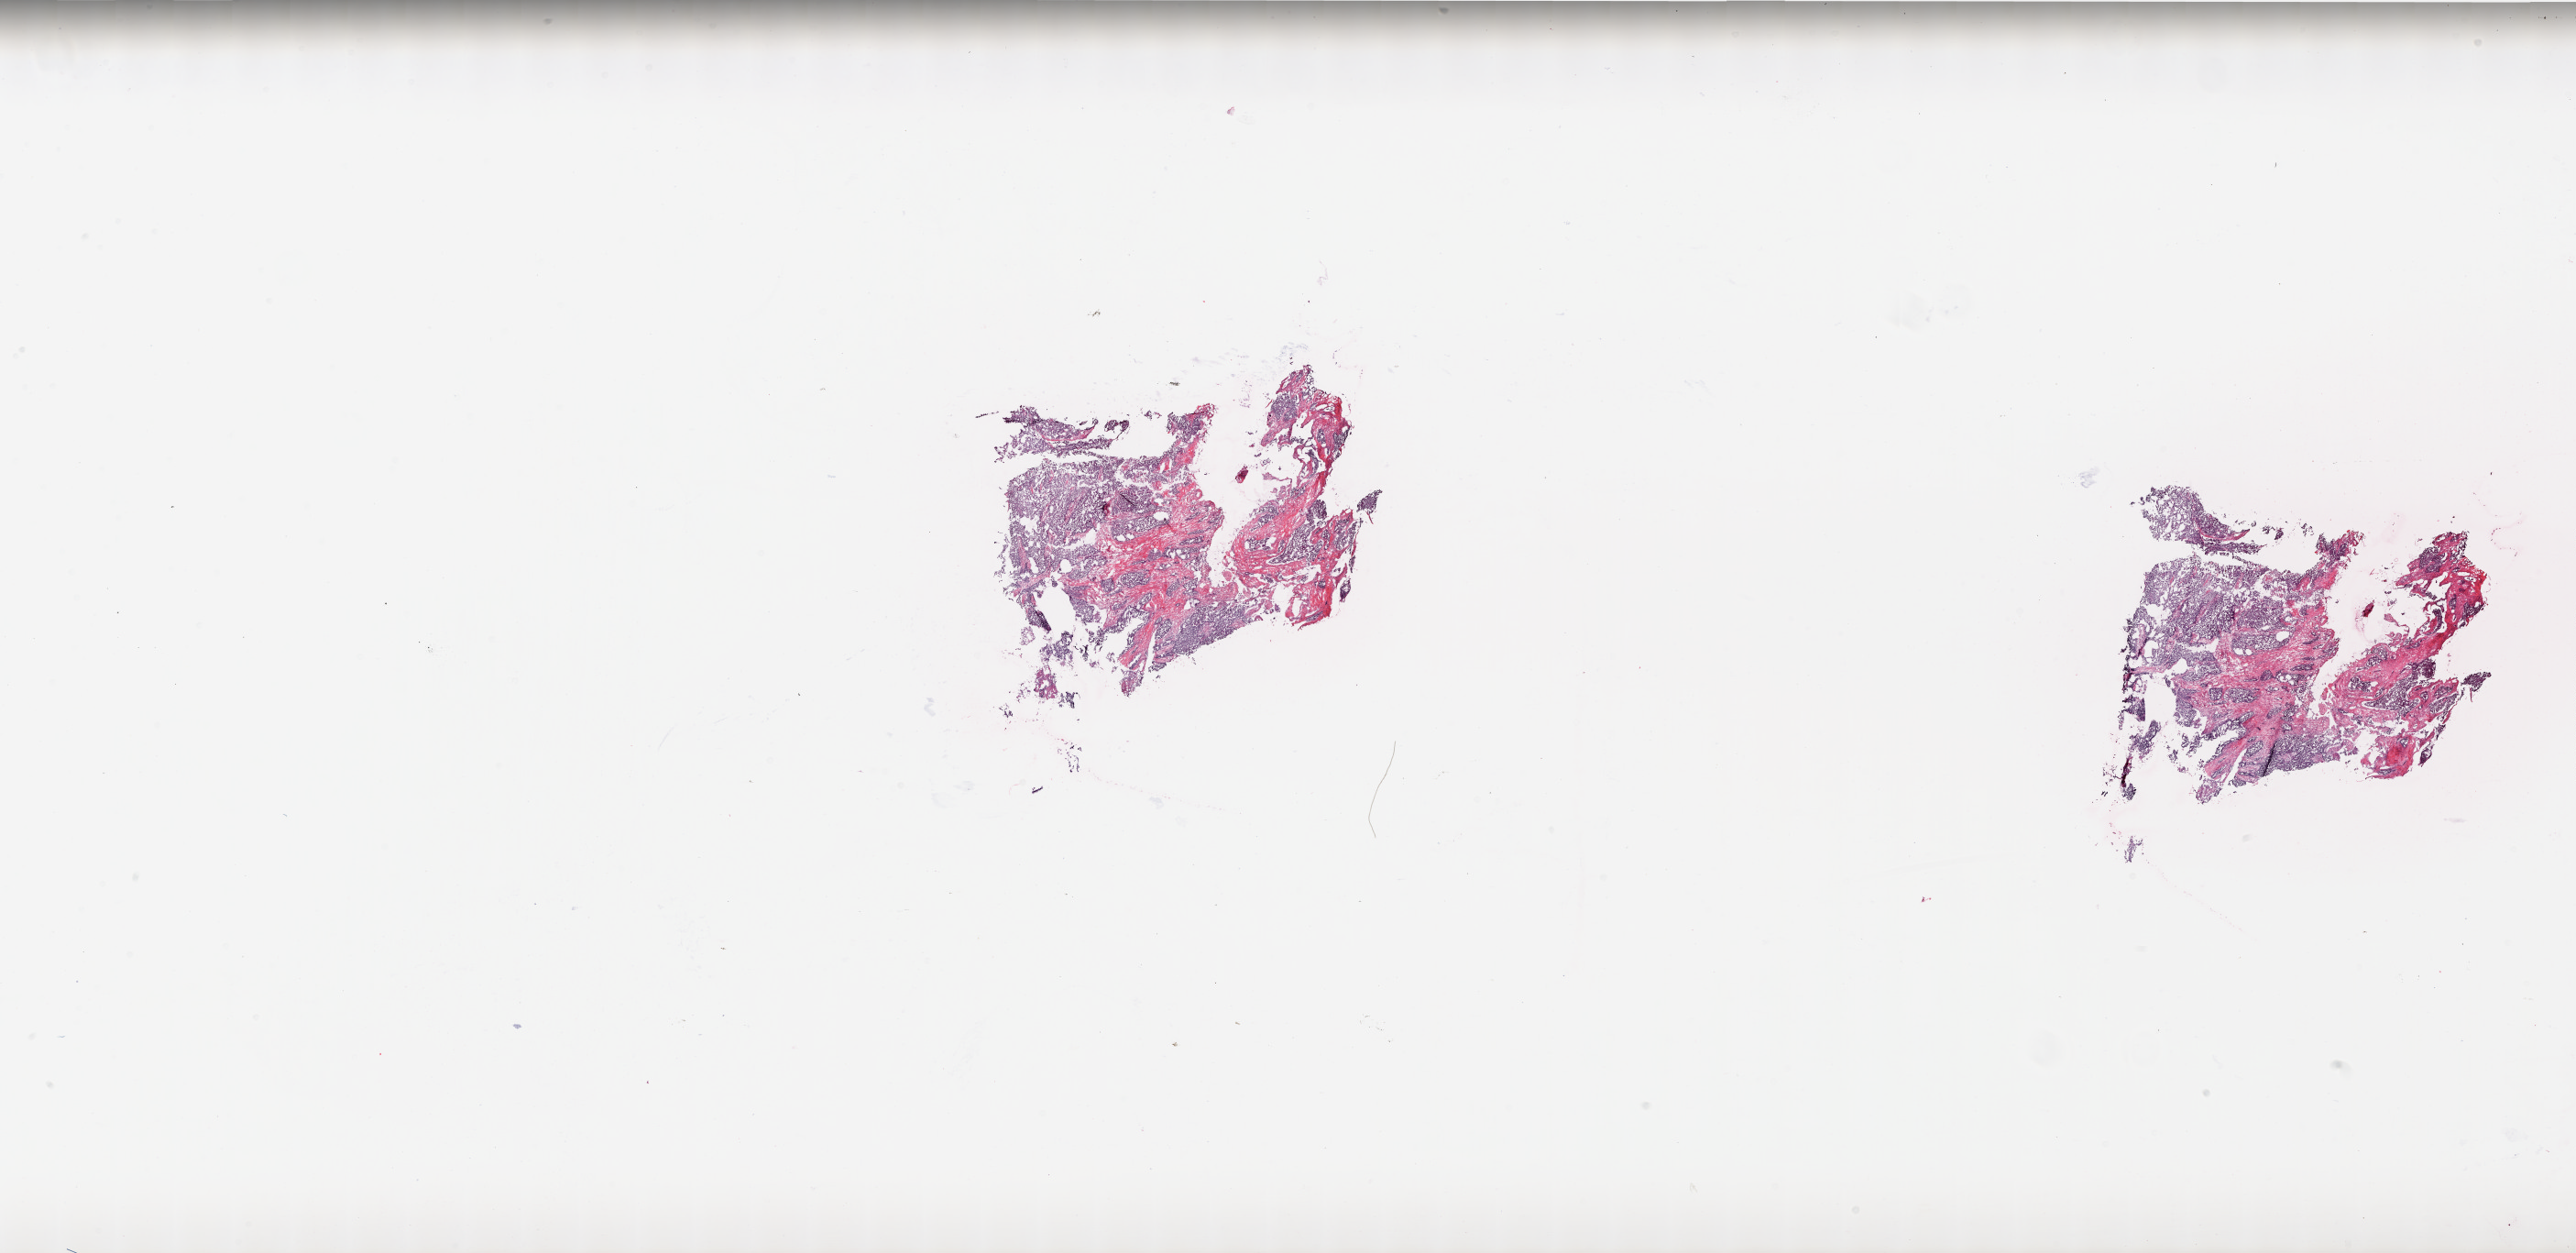
Digitized Hematoxylin and eosin (H&E) stained tissue section (whole slide), a low-resolution overview of the entire scanned area, about 44.9 x 21.8 mm (from a 20x scan); frozen section from the top of the tissue portion; ovary, primary tumour sample. Female, age 60 years at initial diagnosis. Histologic grade: G3 (poorly differentiated). Pathologist review of this section (percent, as recorded): tumour cells 95%, tumour nuclei 95%, normal cells 0%, stromal cells 5%, necrosis 0%.
FIGO stage: IV. Laterality: bilateral. Pathologic diagnosis: Serous cystadenocarcinoma, NOS.